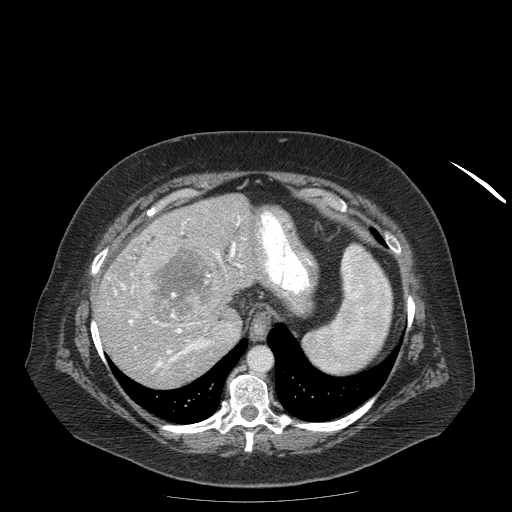
Contrast-enhanced abdominal CT (liver protocol), one axial slice; position 143 of 204 along the scan axis; reconstruction kernel STANDARD; soft-tissue window (W 400 / L 40 HU); 512 × 512 image matrix, field of view 440 × 440 mm. Case-level facts recorded for this patient, not image findings: diagnosis: hepatocellular carcinoma (patient treated with transarterial chemoembolisation; whether this scan precedes or follows treatment is not stated here); TNM stage (as recorded): Stage-IIIB; Child-Pugh class: A; tumour differentiation: well differentiated.
Structures marked on this image (semi-automatic segmentation, software-assisted and operator-edited):
- liver parenchyma outside the tumour (the mass and vessels are separate outlines, so this box may not span the whole liver): bounding box <94,194,266,388> (left, top, right, bottom; pixels)
- mass: <140,236,223,327>
- liver vessels: <107,216,245,372>